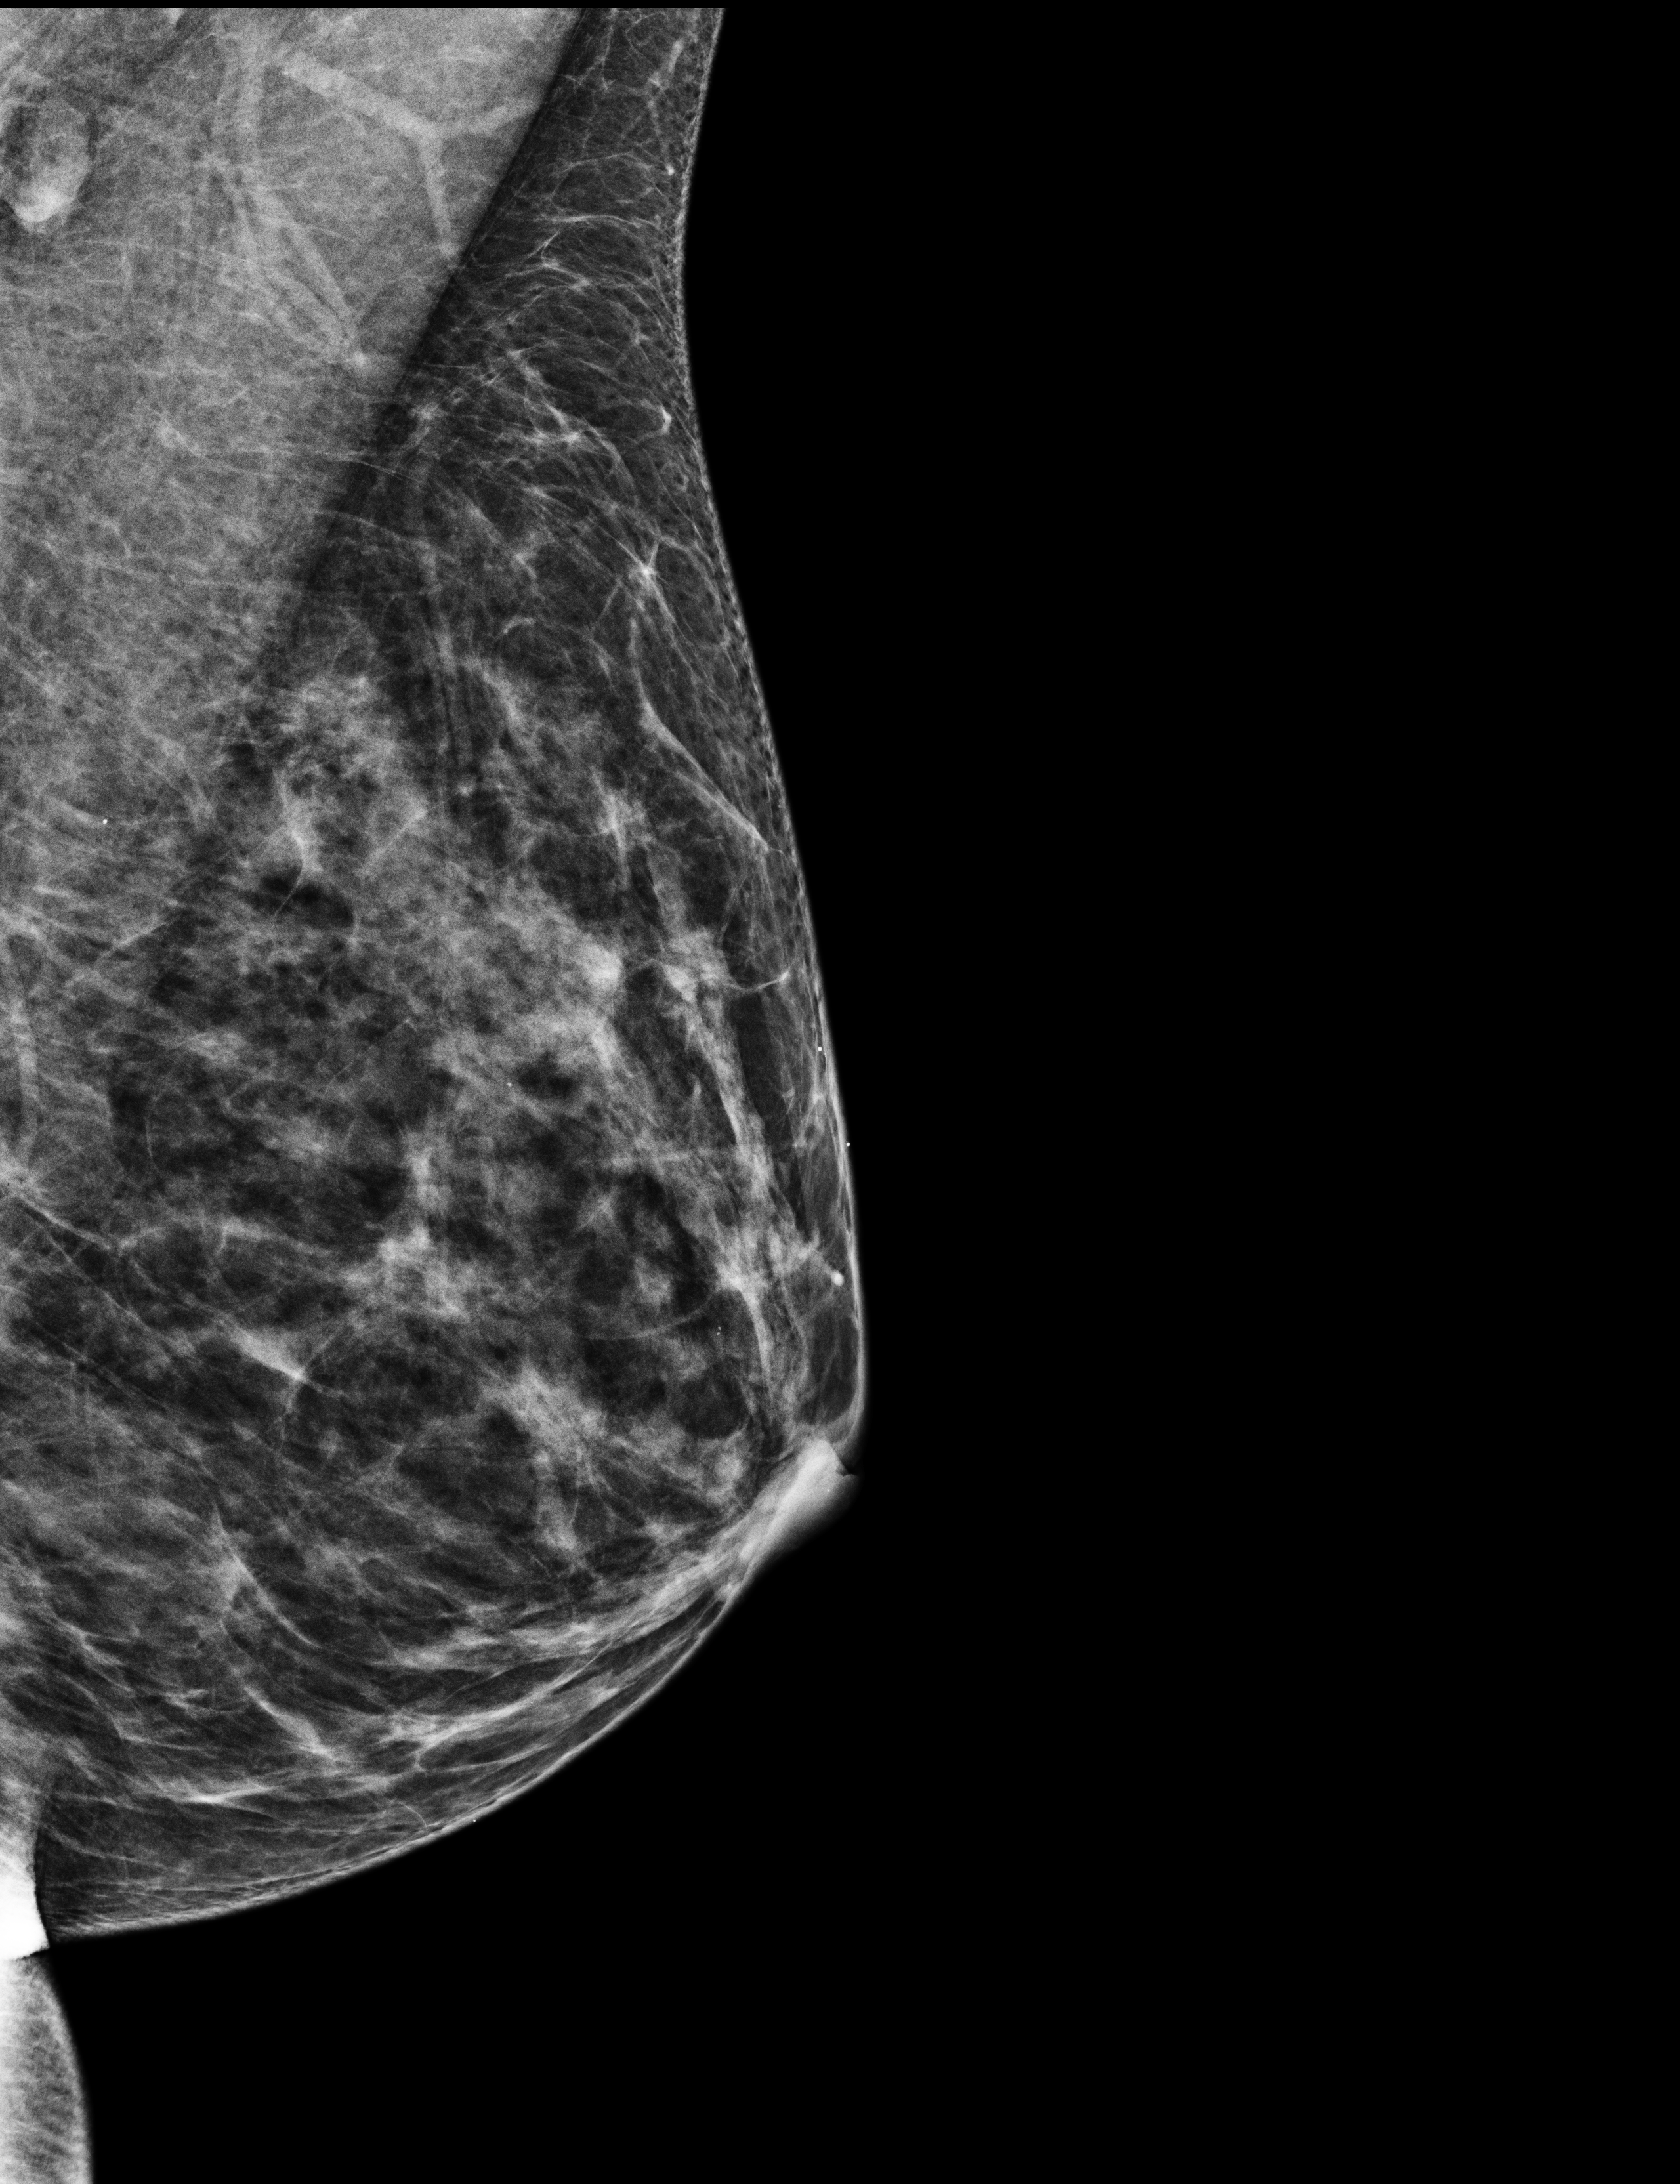
Annual screening mammography examination, compressed breast thickness 40 mm. Patient aged 44 years (female).
Image type: full-field digital mammogram. Breast: left. Projection: MLO view.